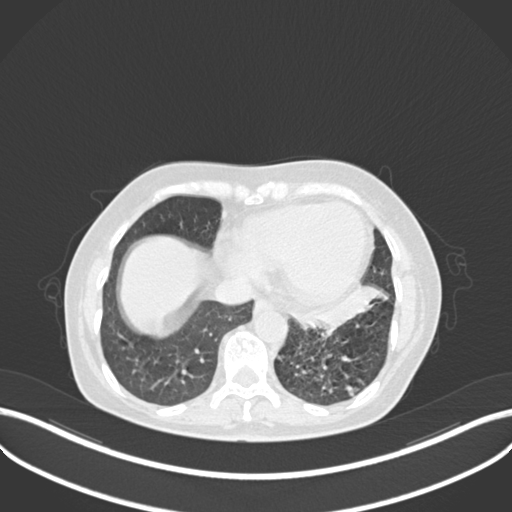
Chest CT, one axial slice. Slice 75 of 270 in the series (ordered by position). 120 kVp. Lung window (W 1500 / L -600 HU). 1 mm slice thickness. 512 × 512 image matrix, field of view 400 × 400 mm. Female patient, age 63 years. Case-level facts recorded for this patient, not image findings: clinical TNM (as recorded): T1b N0 M0; histopathological grade: G2-3.
Outlined on this slice (bounding box drawn by a radiologist):
- lung tumour (recorded histology: adenocarcinoma): box from (x=298, y=285) to (x=390, y=340) px